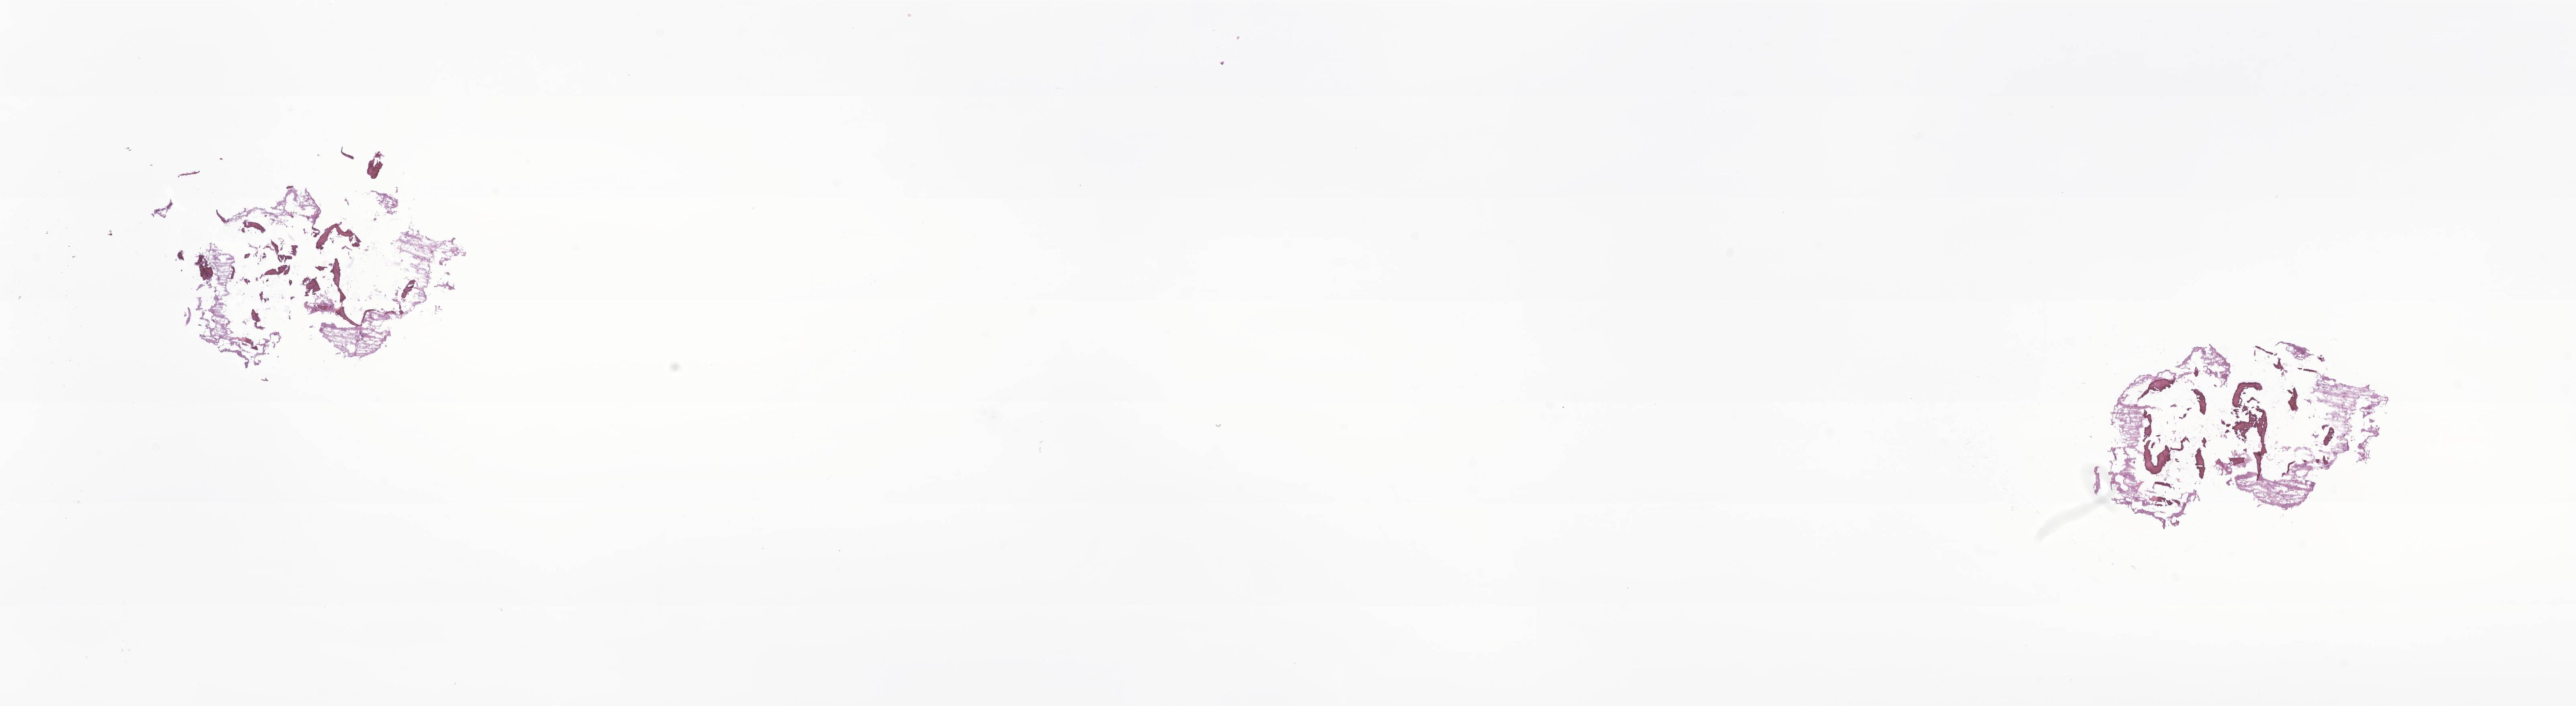
Whole-slide image, H&E stain of tumor tissue from the cerebellum — low-resolution overview of the scanned area, about 27.0 x 7.4 mm; frozen section. Male patient, age 78 months (6 years 6 months).
Diagnosis (ICD-O-3 morphology term): Pilocytic astrocytoma.